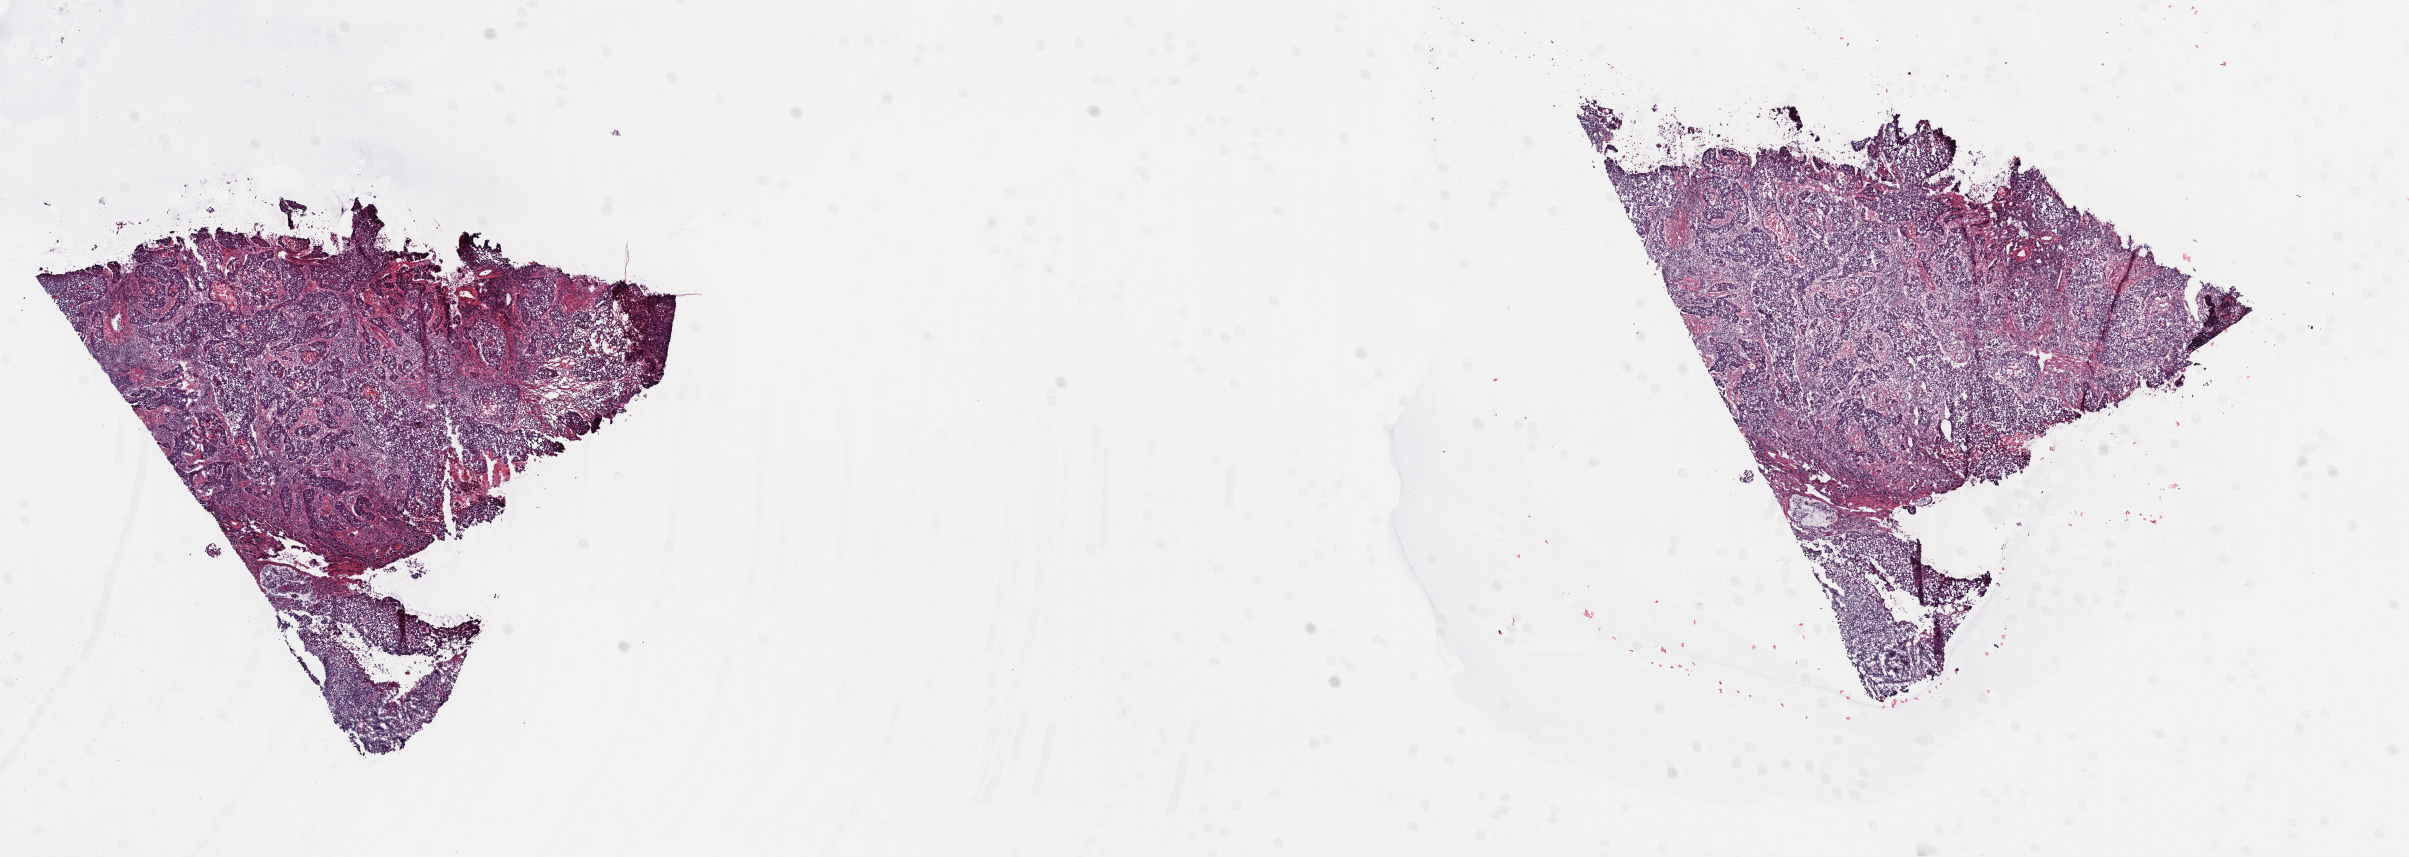
Hematoxylin and eosin (H&E) stained whole-slide image, a low-resolution overview of the entire scanned area, about 18.9 x 6.7 mm (acquisition: 40x scan). Frozen section from the top of the tissue portion. Primary tumour sample from the cervix. Female, age 37 years at initial diagnosis. Histologic grade: G3 (poorly differentiated). Composition of this section per pathologist review: tumour cells 60%, tumour nuclei 60%, normal cells 20%, stromal cells 20%, necrosis 0%. Infiltration values recorded for this section: lymphocyte infiltration 5%, monocyte infiltration 0%, neutrophil infiltration 5%.
• lymph nodes positive (case pathology): 0 of 13 examined
• FIGO stage: IB1
• pathologic diagnosis: Squamous cell carcinoma, keratinizing, NOS (cervix uteri)